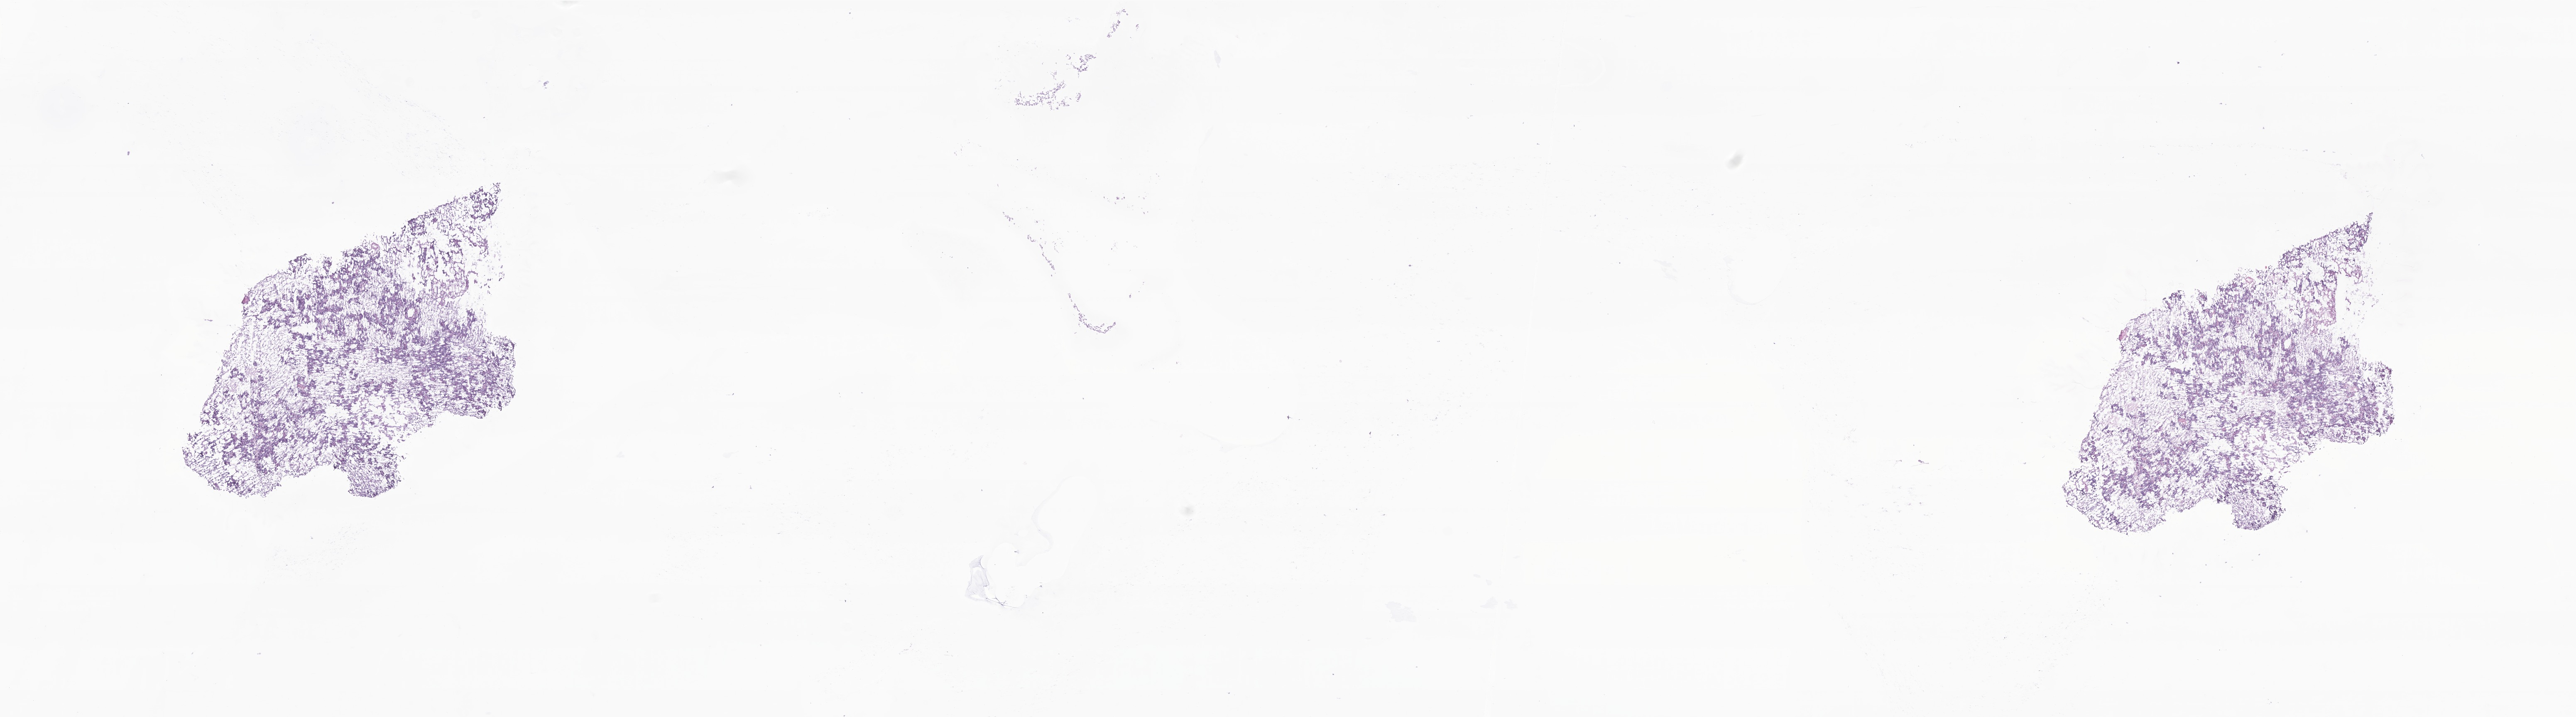
Digitized haematoxylin and eosin-stained section of tumor tissue from the brain — low-resolution overview of the scanned area, about 26.2 x 7.3 mm. Frozen section (OCT-embedded). Patient: male, age 39 months.
• recorded diagnosis: Medulloblastoma, NOS